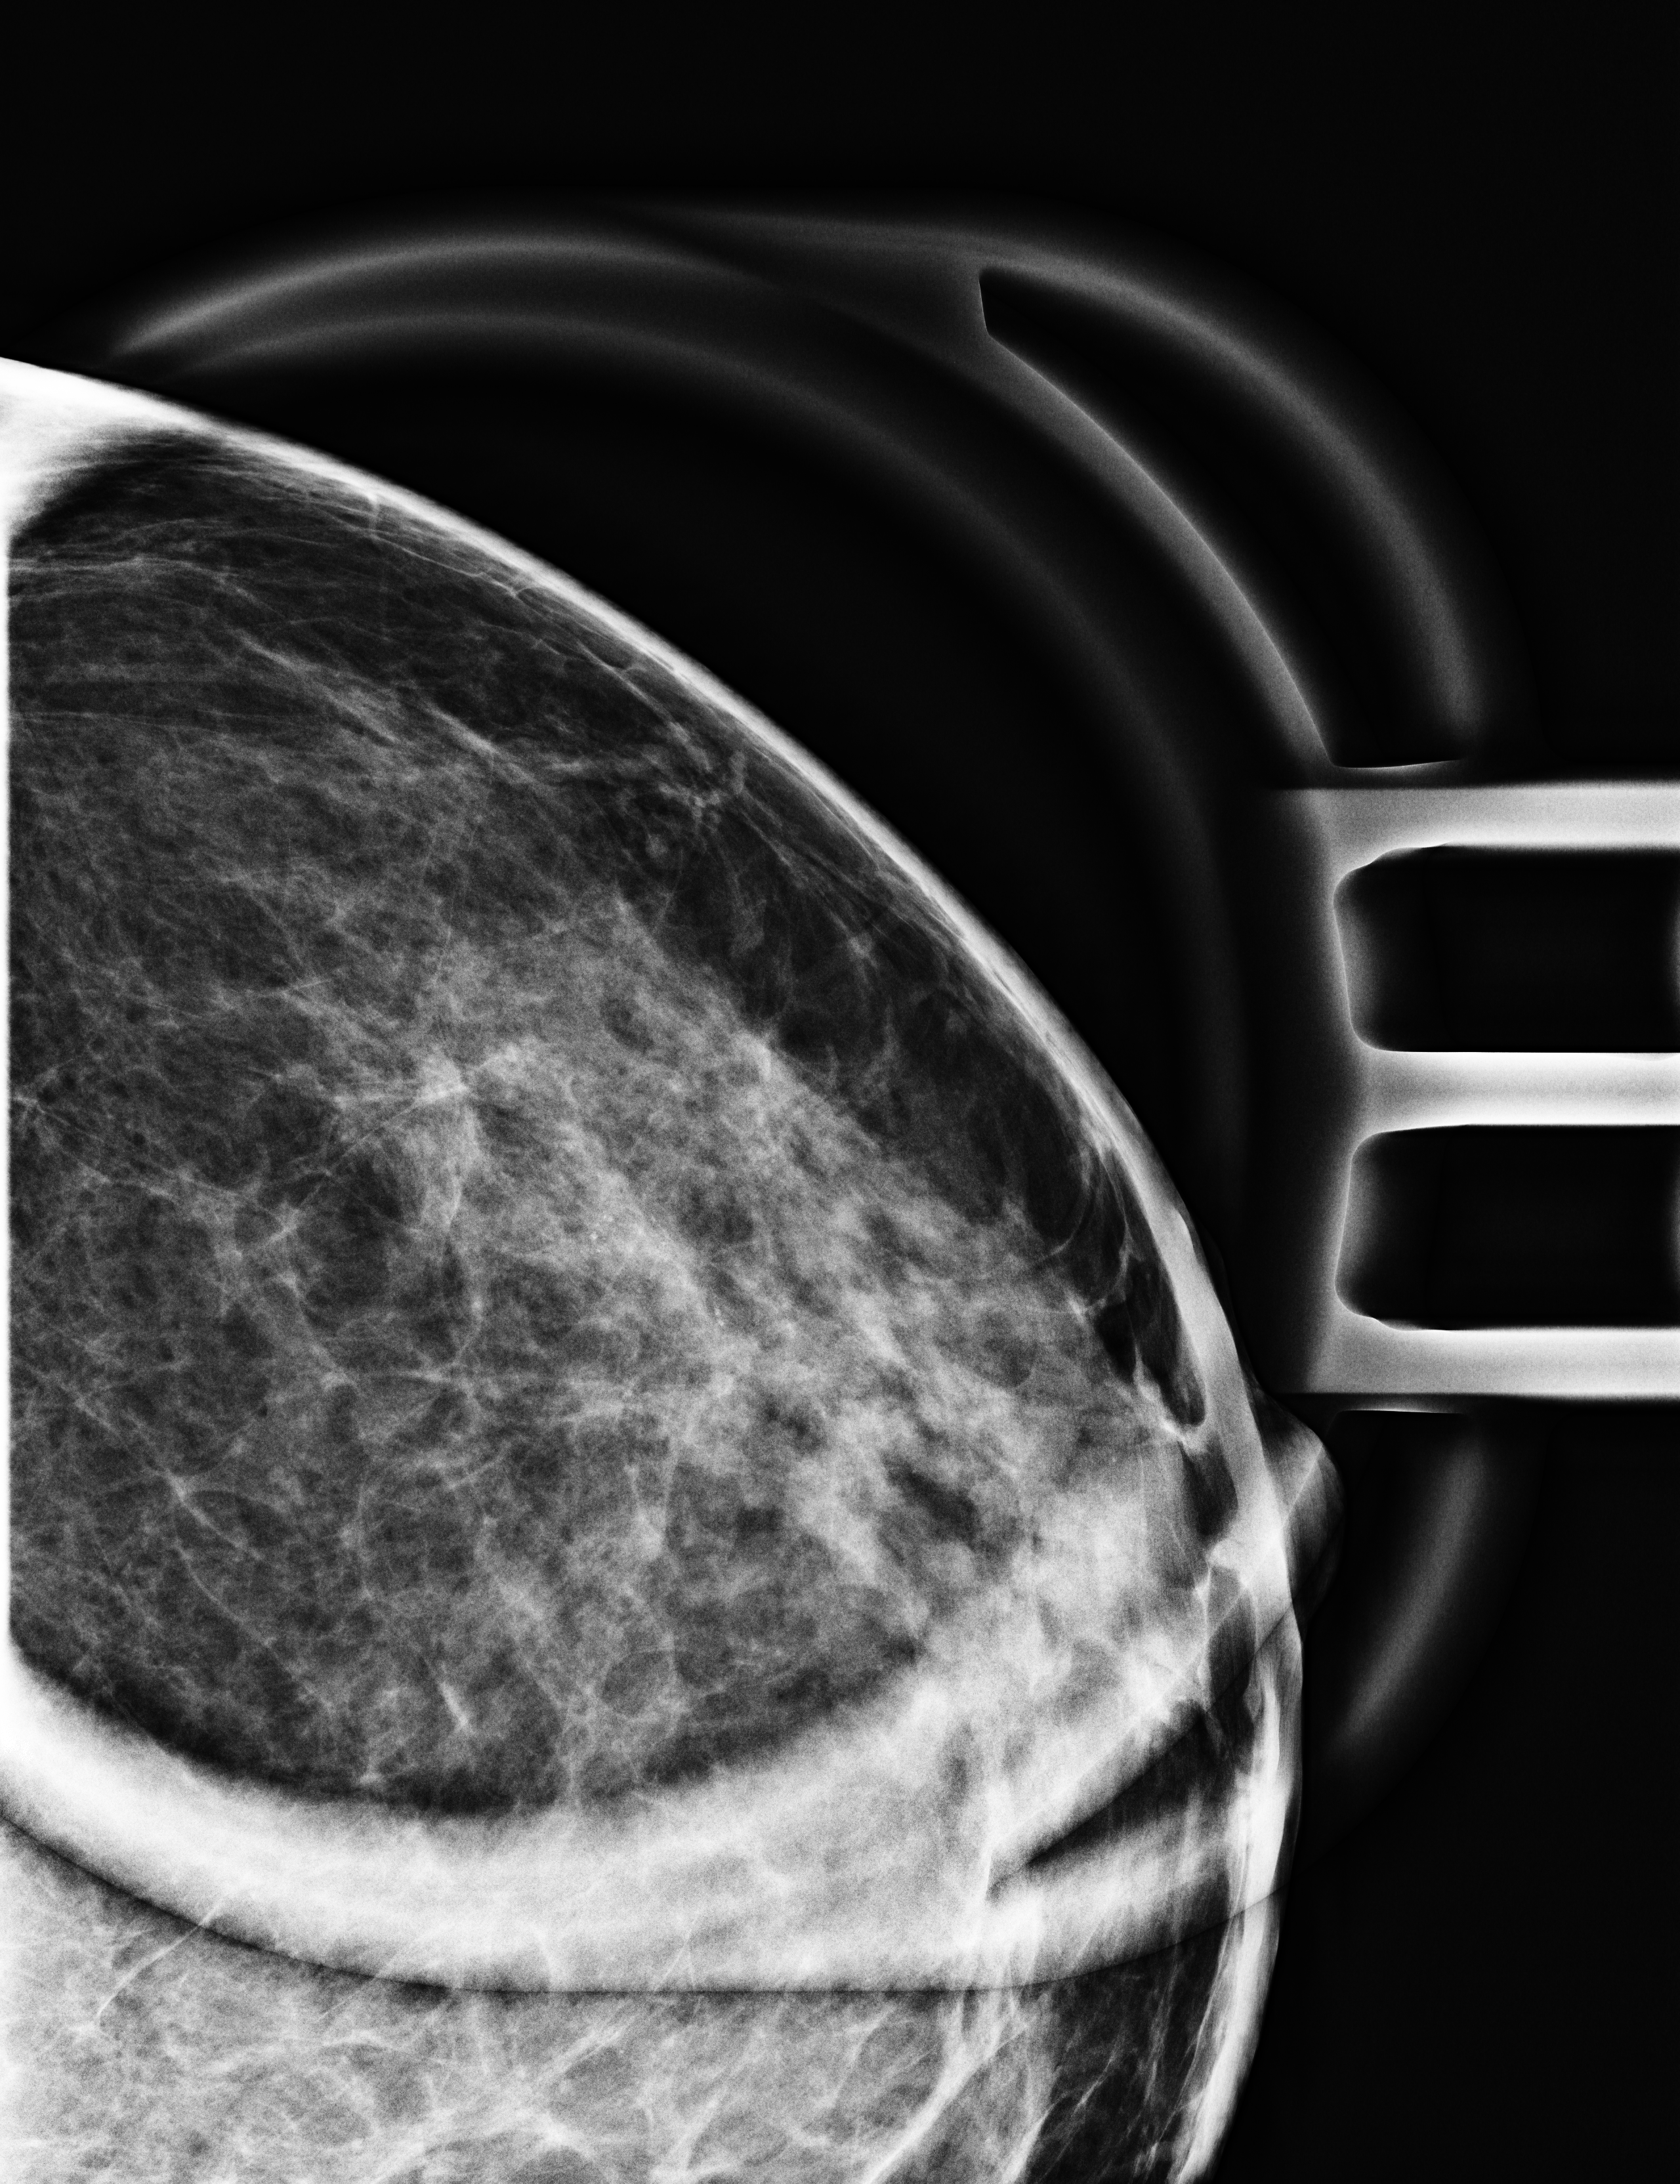
Additional (diagnostic) view, system: Selenia Dimensions. Female patient, age 46 years.
Image type: full-field digital mammogram. Breast: left. Projection: craniocaudal (CC) view, magnification.